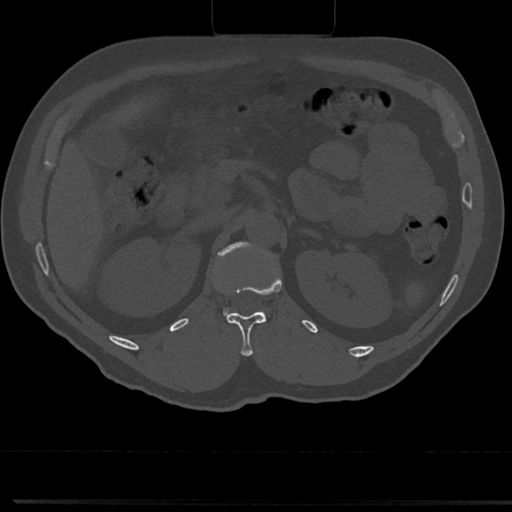
CT including the spine, one axial slice. Position 121 of 817 along the scan axis. Reconstruction kernel Br40s/3. 120 kVp. Bone window (W 1800 / L 400 HU). 0.5 mm slice thickness. 512 × 512 image matrix, field of view 355 × 355 mm. Male patient, age 61 years. Case-level facts recorded for this patient, not image findings: primary cancer: prostate.
Annotated regions visible in this slice (semi-automatically segmented with operator editing):
- L1 vertebra: bounding box (x1, y1, x2, y2) in pixels: (212, 241, 276, 322)
- T12 vertebra: (224, 311, 267, 355)